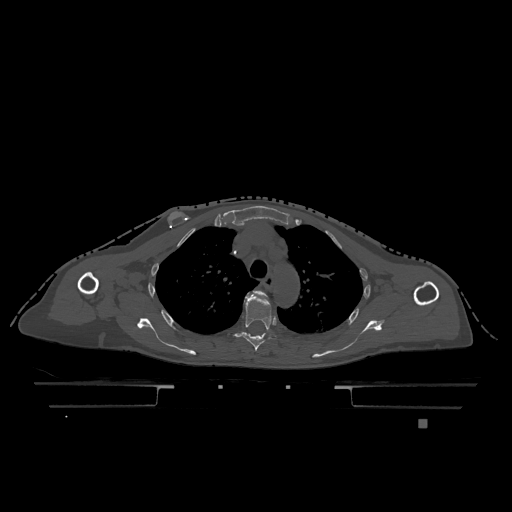
CT including the spine, one axial slice. Slice 883 of 1317 in the series (ordered by position). Bone window (W 1800 / L 400 HU). 0.5 mm slice thickness. 512 × 512 image matrix. Female patient, age 74 years. From the clinical record (not read from this slice): primary cancer: lung.
Outlined on this slice (semi-automatic segmentation, software-assisted and operator-edited):
- T3 vertebra: bounding box (x1, y1, x2, y2) in pixels: (253, 291, 267, 298)
- T4 vertebra: (235, 292, 277, 351)